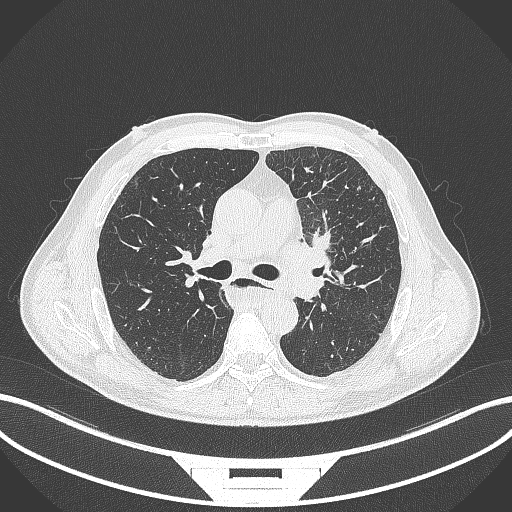
Chest CT, one axial slice; slice 232 of 411 in the series (ordered by position); 120 kVp; lung window (W 1500 / L -600 HU); 1 mm slice thickness; 512 × 512 image matrix, field of view 400 × 400 mm. Patient: male, 57 years. From the clinical record (not read from this slice): clinical TNM (as recorded): T2a N1 M0.
Annotated regions visible in this slice (rectangle marked by the reading radiologist):
- lung tumour (recorded histology: squamous cell carcinoma): bounding box (x1, y1, x2, y2) in pixels: (283, 232, 344, 310)